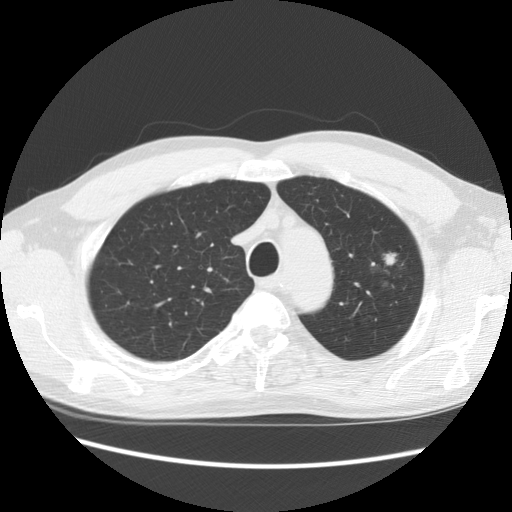
Low-dose screening chest CT, axial slice, second screening round (one year after baseline), lung window (W 1500 / L -600 HU), 2.5 mm slice thickness, standard (soft-tissue) reconstruction kernel (STANDARD), slice 109 of 139 in the series, 512 × 512 image matrix. Male, age 61 years at enrolment. Former smoker at enrolment.
Lesion marked by an expert reader, bounding box [x1, y1, x2, y2] px = [341, 222, 428, 303]. The exam's reader record, not a measurement of the box and not confirmed to be the same lesion: non-calcified nodule or mass ≥4 mm, left upper lobe, 34 × 32 mm, poorly defined margins, mixed attenuation, pre-existing on the prior screen: yes; interval growth: no. Participant outcome: lung cancer diagnosed 704 days after this screen (after the third annual screen) — bronchiolo-alveolar adenocarcinoma, NOS, left upper lobe, well differentiated (G1), stage IB (AJCC 6th edition), 44 mm at pathology.